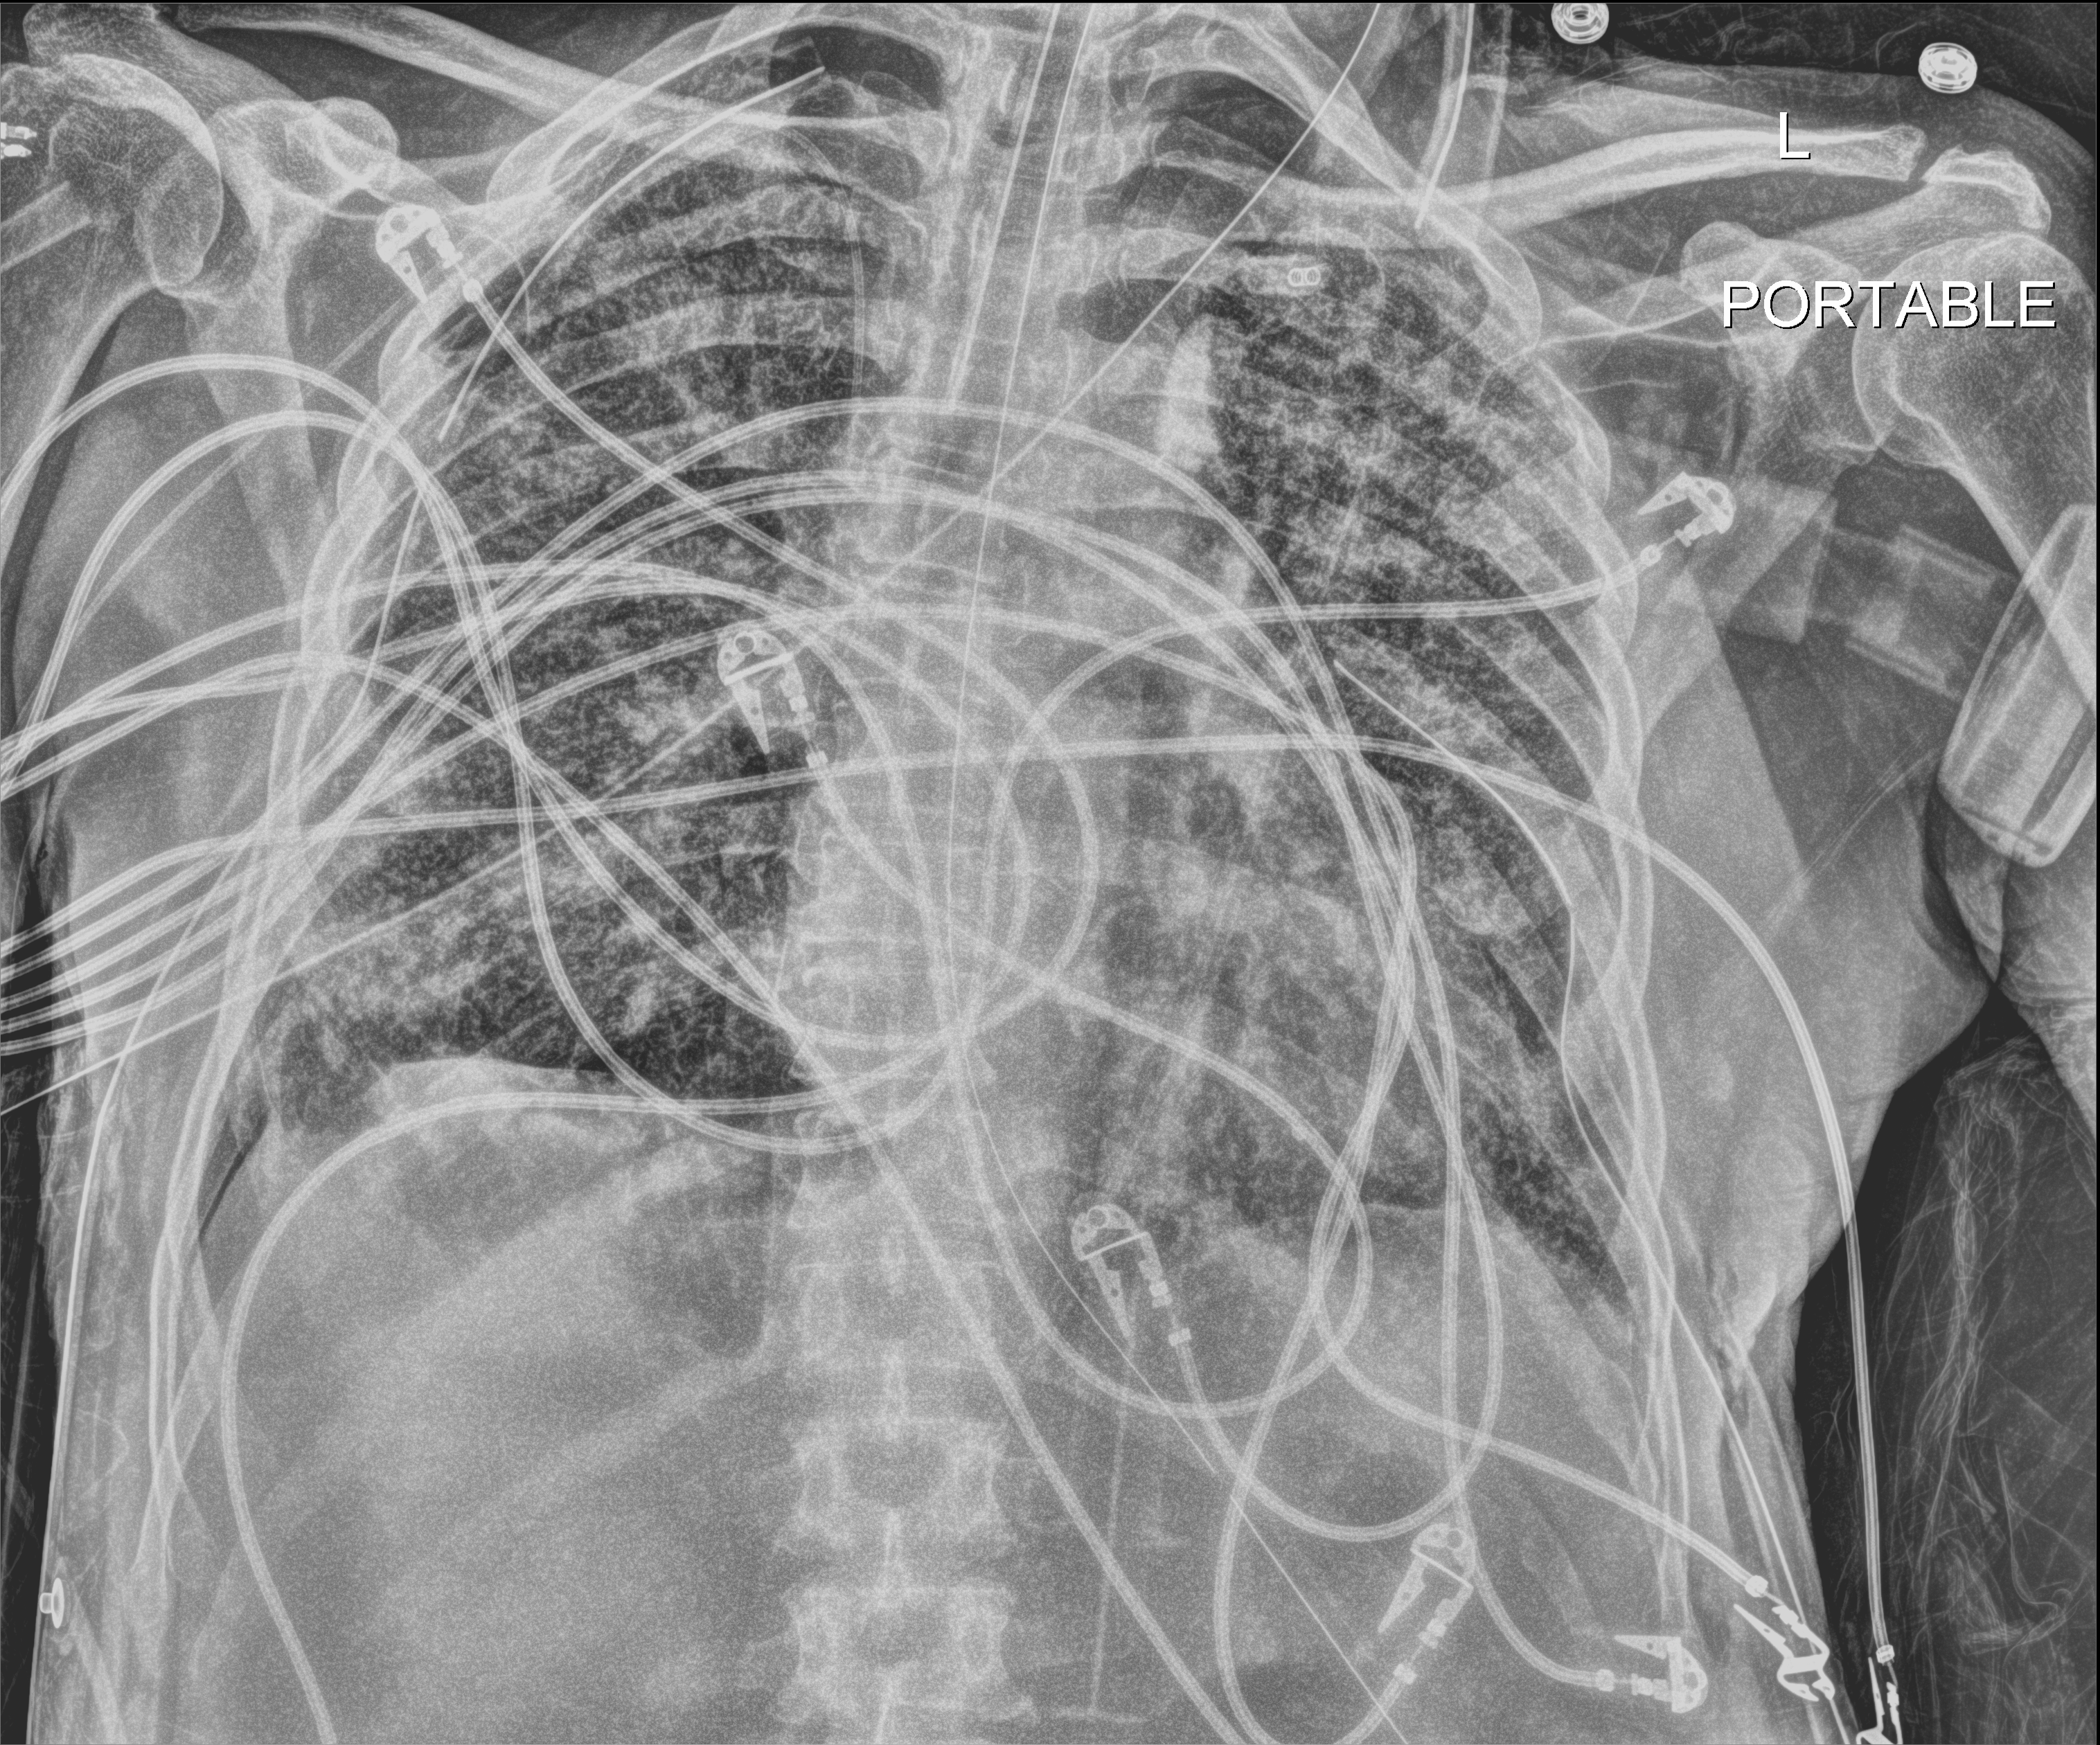
Chest X-ray (portable); anteroposterior (AP) projection. Male patient hospitalised with COVID-19, age 60–74 years.
Admission-level facts for this patient (not findings on this image; timing relative to this image not recorded): mechanically ventilated during this hospital stay: yes; admitted to intensive care during this hospital stay: yes; diabetes (admission record): no.